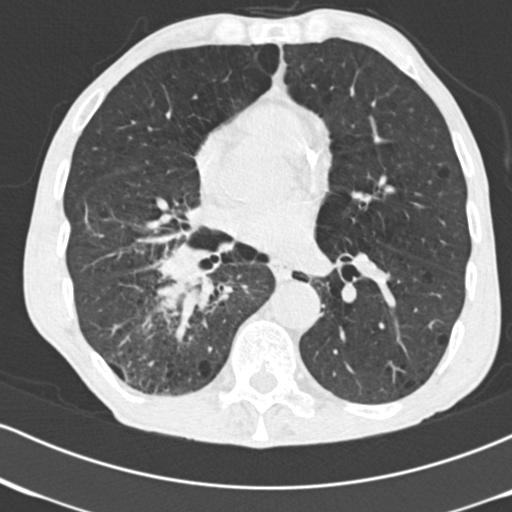
Chest CT (low-dose screening protocol), one axial image. Second annual screen. Lung window (W 1500 / L -600 HU). 2 mm slice thickness. Standard (soft-tissue) reconstruction kernel (B30f). 512 × 512 image matrix. Male, age 64 years at enrolment. Current smoker at enrolment.
Expert reader's lesion annotation, bounding box [x1, y1, x2, y2] px = [125, 225, 243, 337]. The exam's reader record, not a measurement of the box and not confirmed to be the same lesion: non-calcified nodule or mass ≥4 mm, 52 × 37 mm, spiculated (stellate) margins, soft tissue attenuation, pre-existing on the prior screen: no.